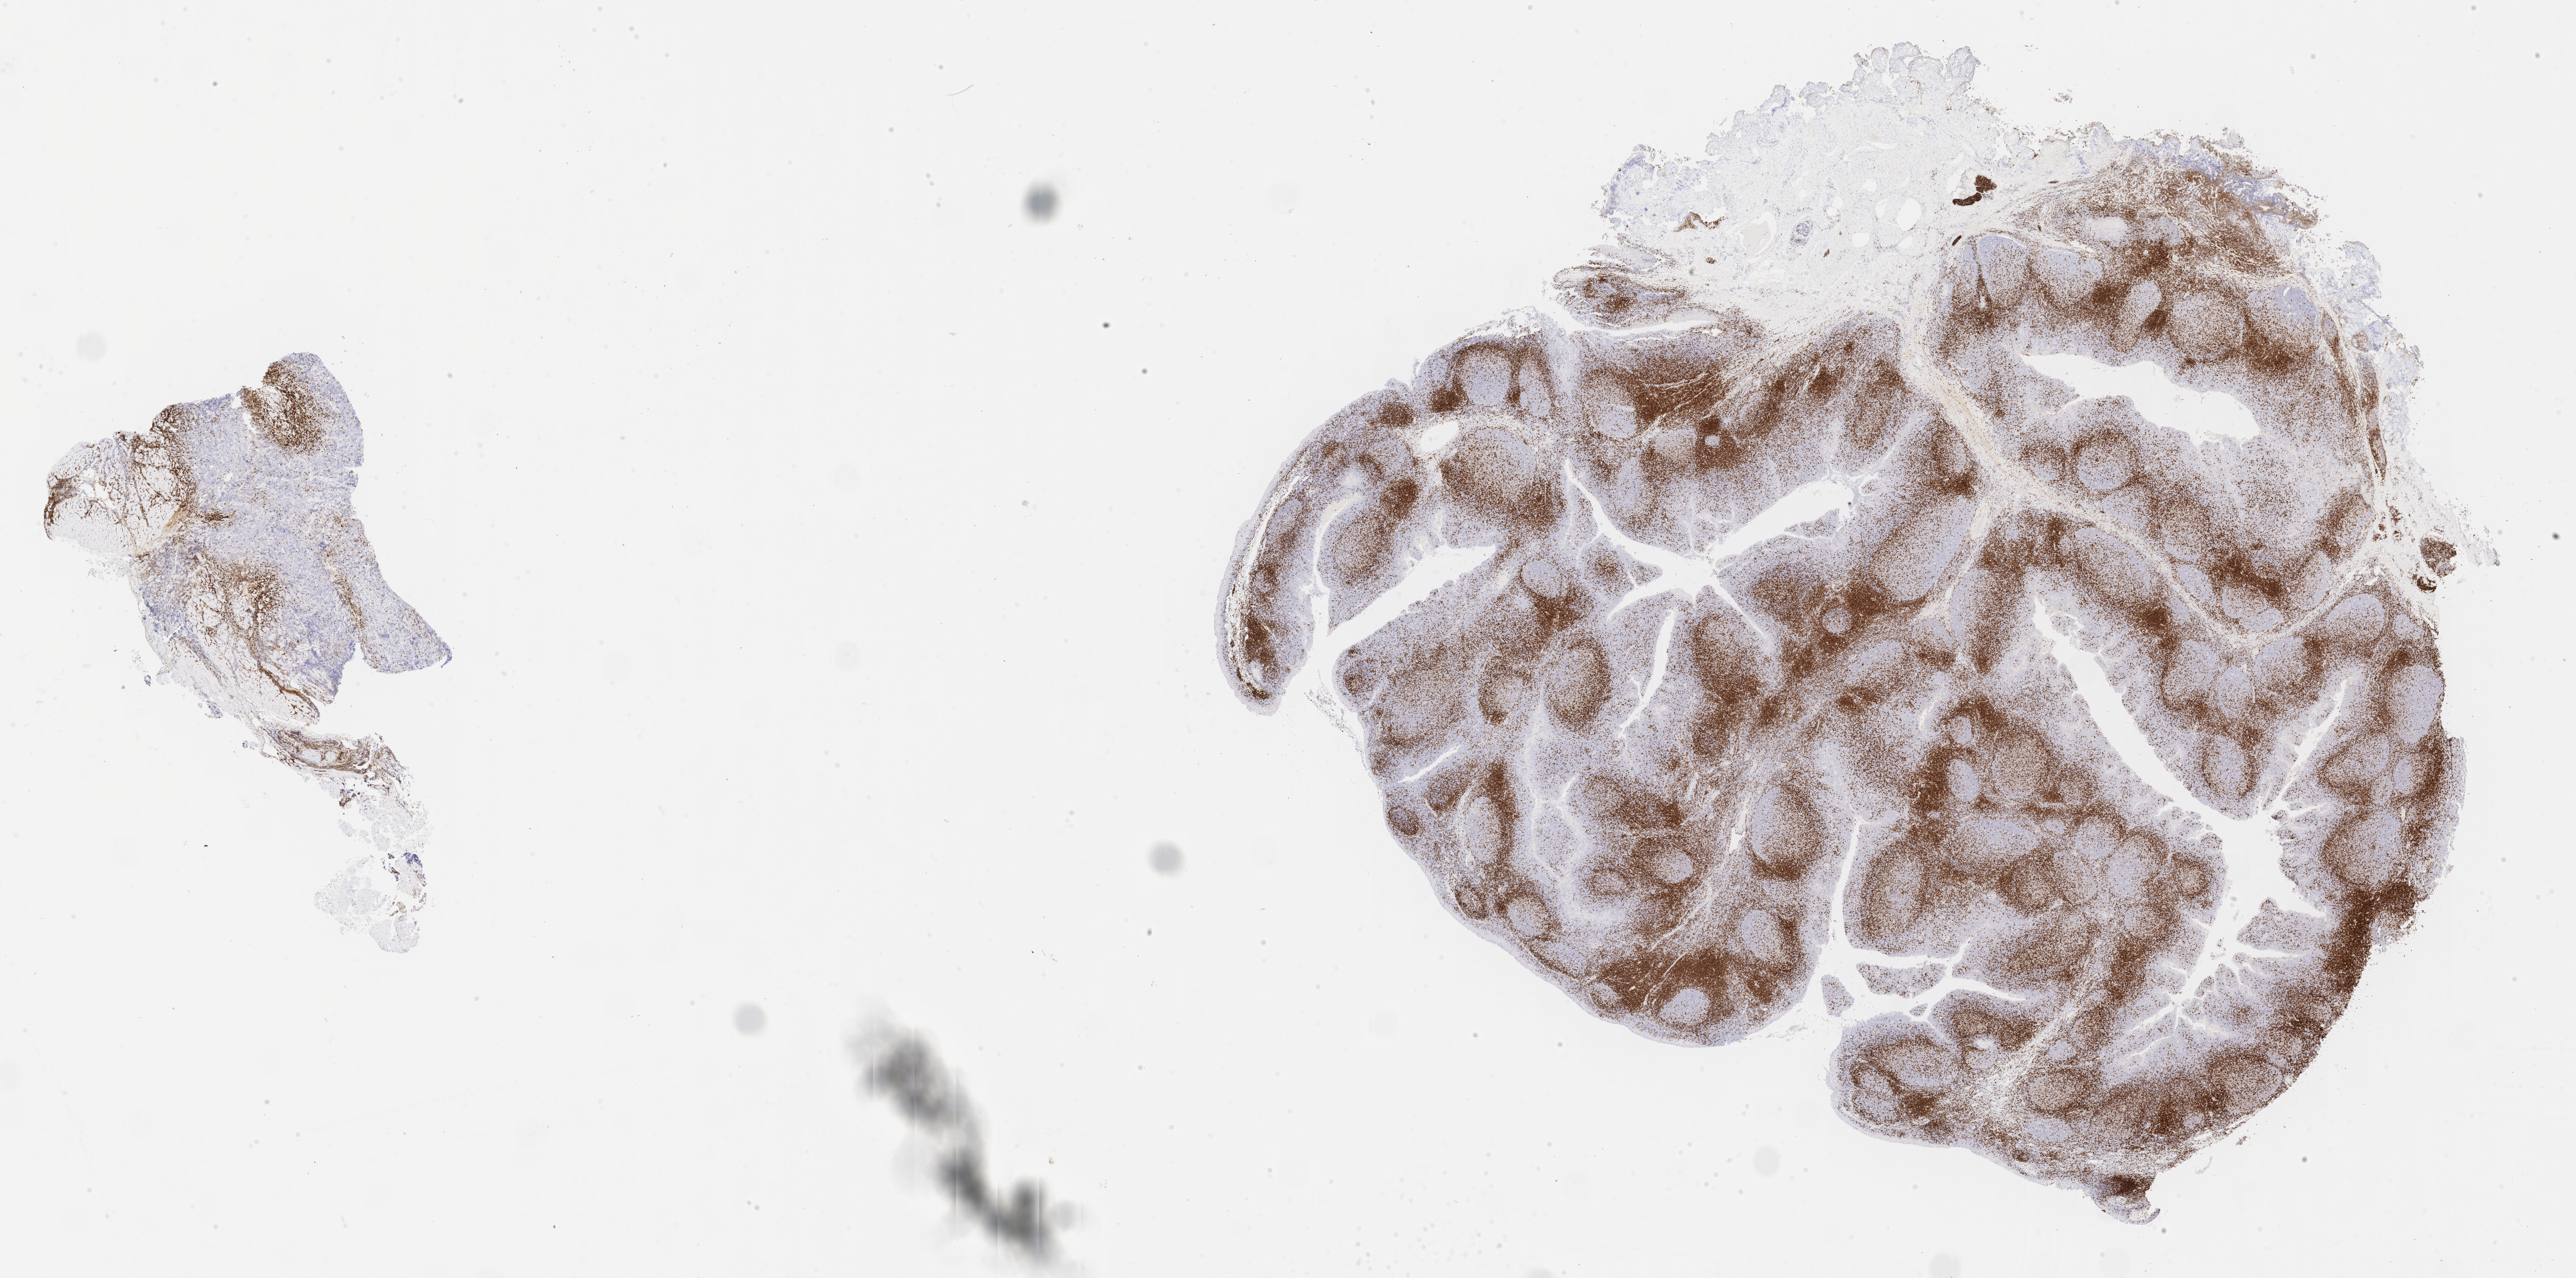
IHC for CD3, whole-slide image, shown as a low-resolution overview of the whole scanned area (about 31.2 x 15.5 mm), specimen: tumor tissue, anatomic site: kidney. Patient: male, age 12 years.
* histologic diagnosis: Diffuse large B-cell lymphoma, NOS